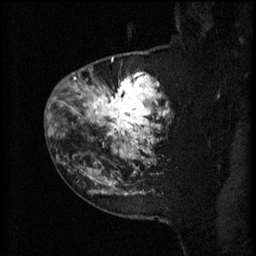
Breast MRI (dynamic contrast-enhanced), one sagittal slice; slice 46 of 60 in the series (ordered by position); 3 images stored at this slice position (order not interpretable as contrast timing); 1.5 T; TE 4.2 ms, TR 11 ms; 2 mm slice thickness; 256 × 256 image matrix, field of view 180 × 180 mm. Patient: female, 52 years.
Annotated regions visible in this slice (semi-automatically segmented with operator editing):
- analysis volume of interest (the breast-tissue region the enhancement analysis was run in; not a lesion): box from (x=81, y=52) to (x=173, y=157) px
- tumour enhancement mask (voxels above the 70 % enhancement threshold inside the analysis volume of interest): (x=81, y=58)–(x=171, y=157)